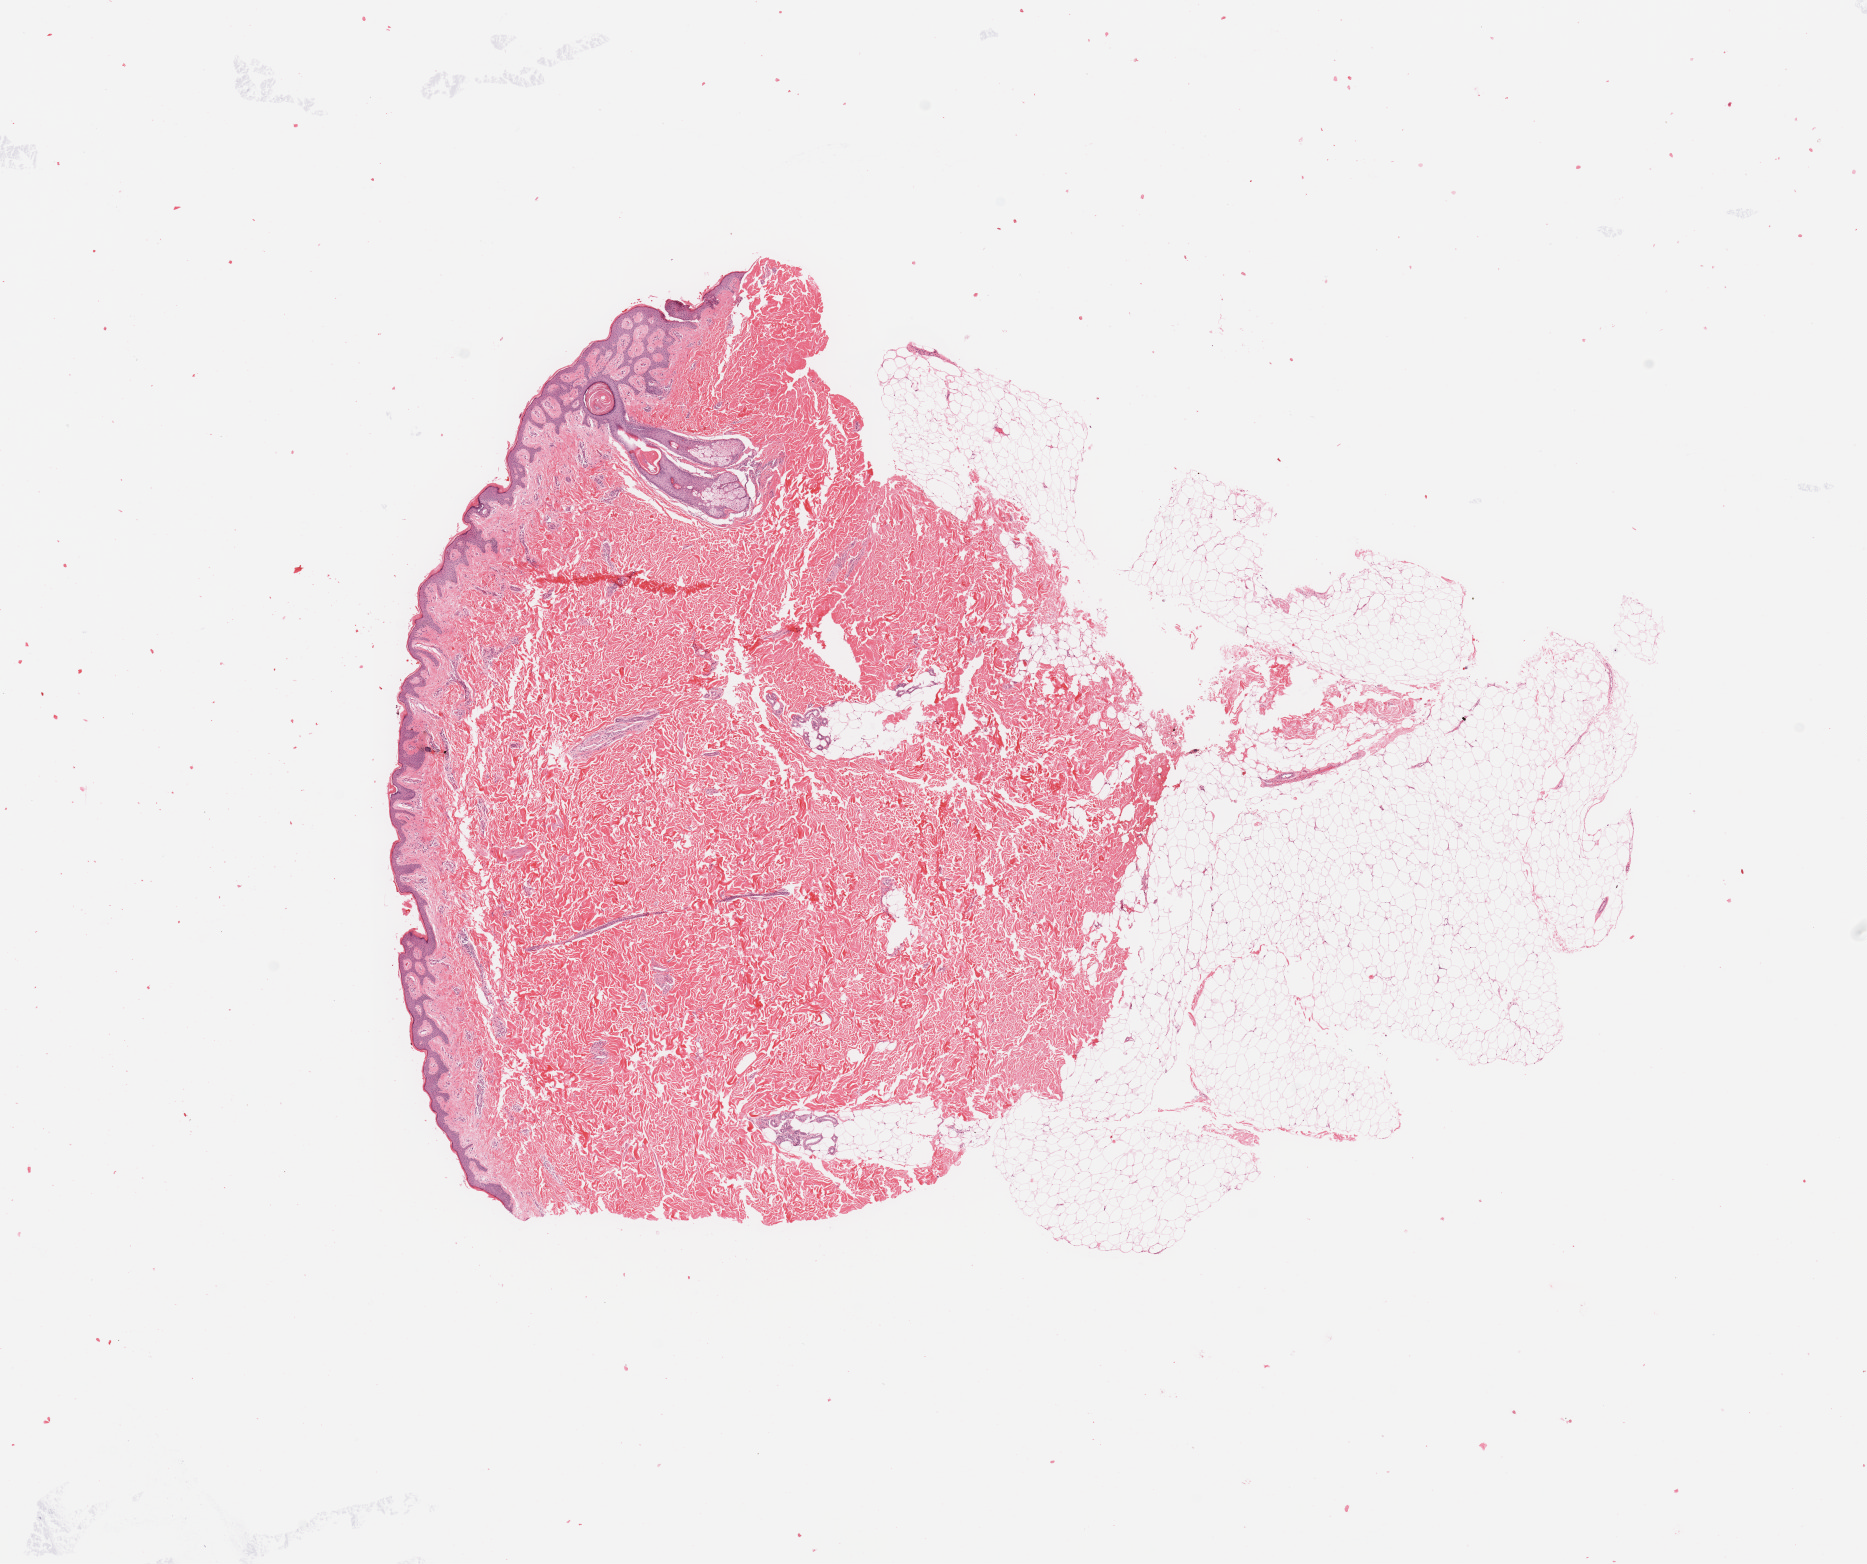
Digitized H&E tissue section (whole slide) — low-resolution overview of the scanned area, about 14.8 x 12.4 mm (slide scanned at 20x); normal (non-tumour) tissue (melanoma cohort); sampled site not recorded. Patient: male, age 34 years.
This section: normal (non-tumour) tissue from the same patient. Patient diagnosis: Malignant melanoma, NOS.